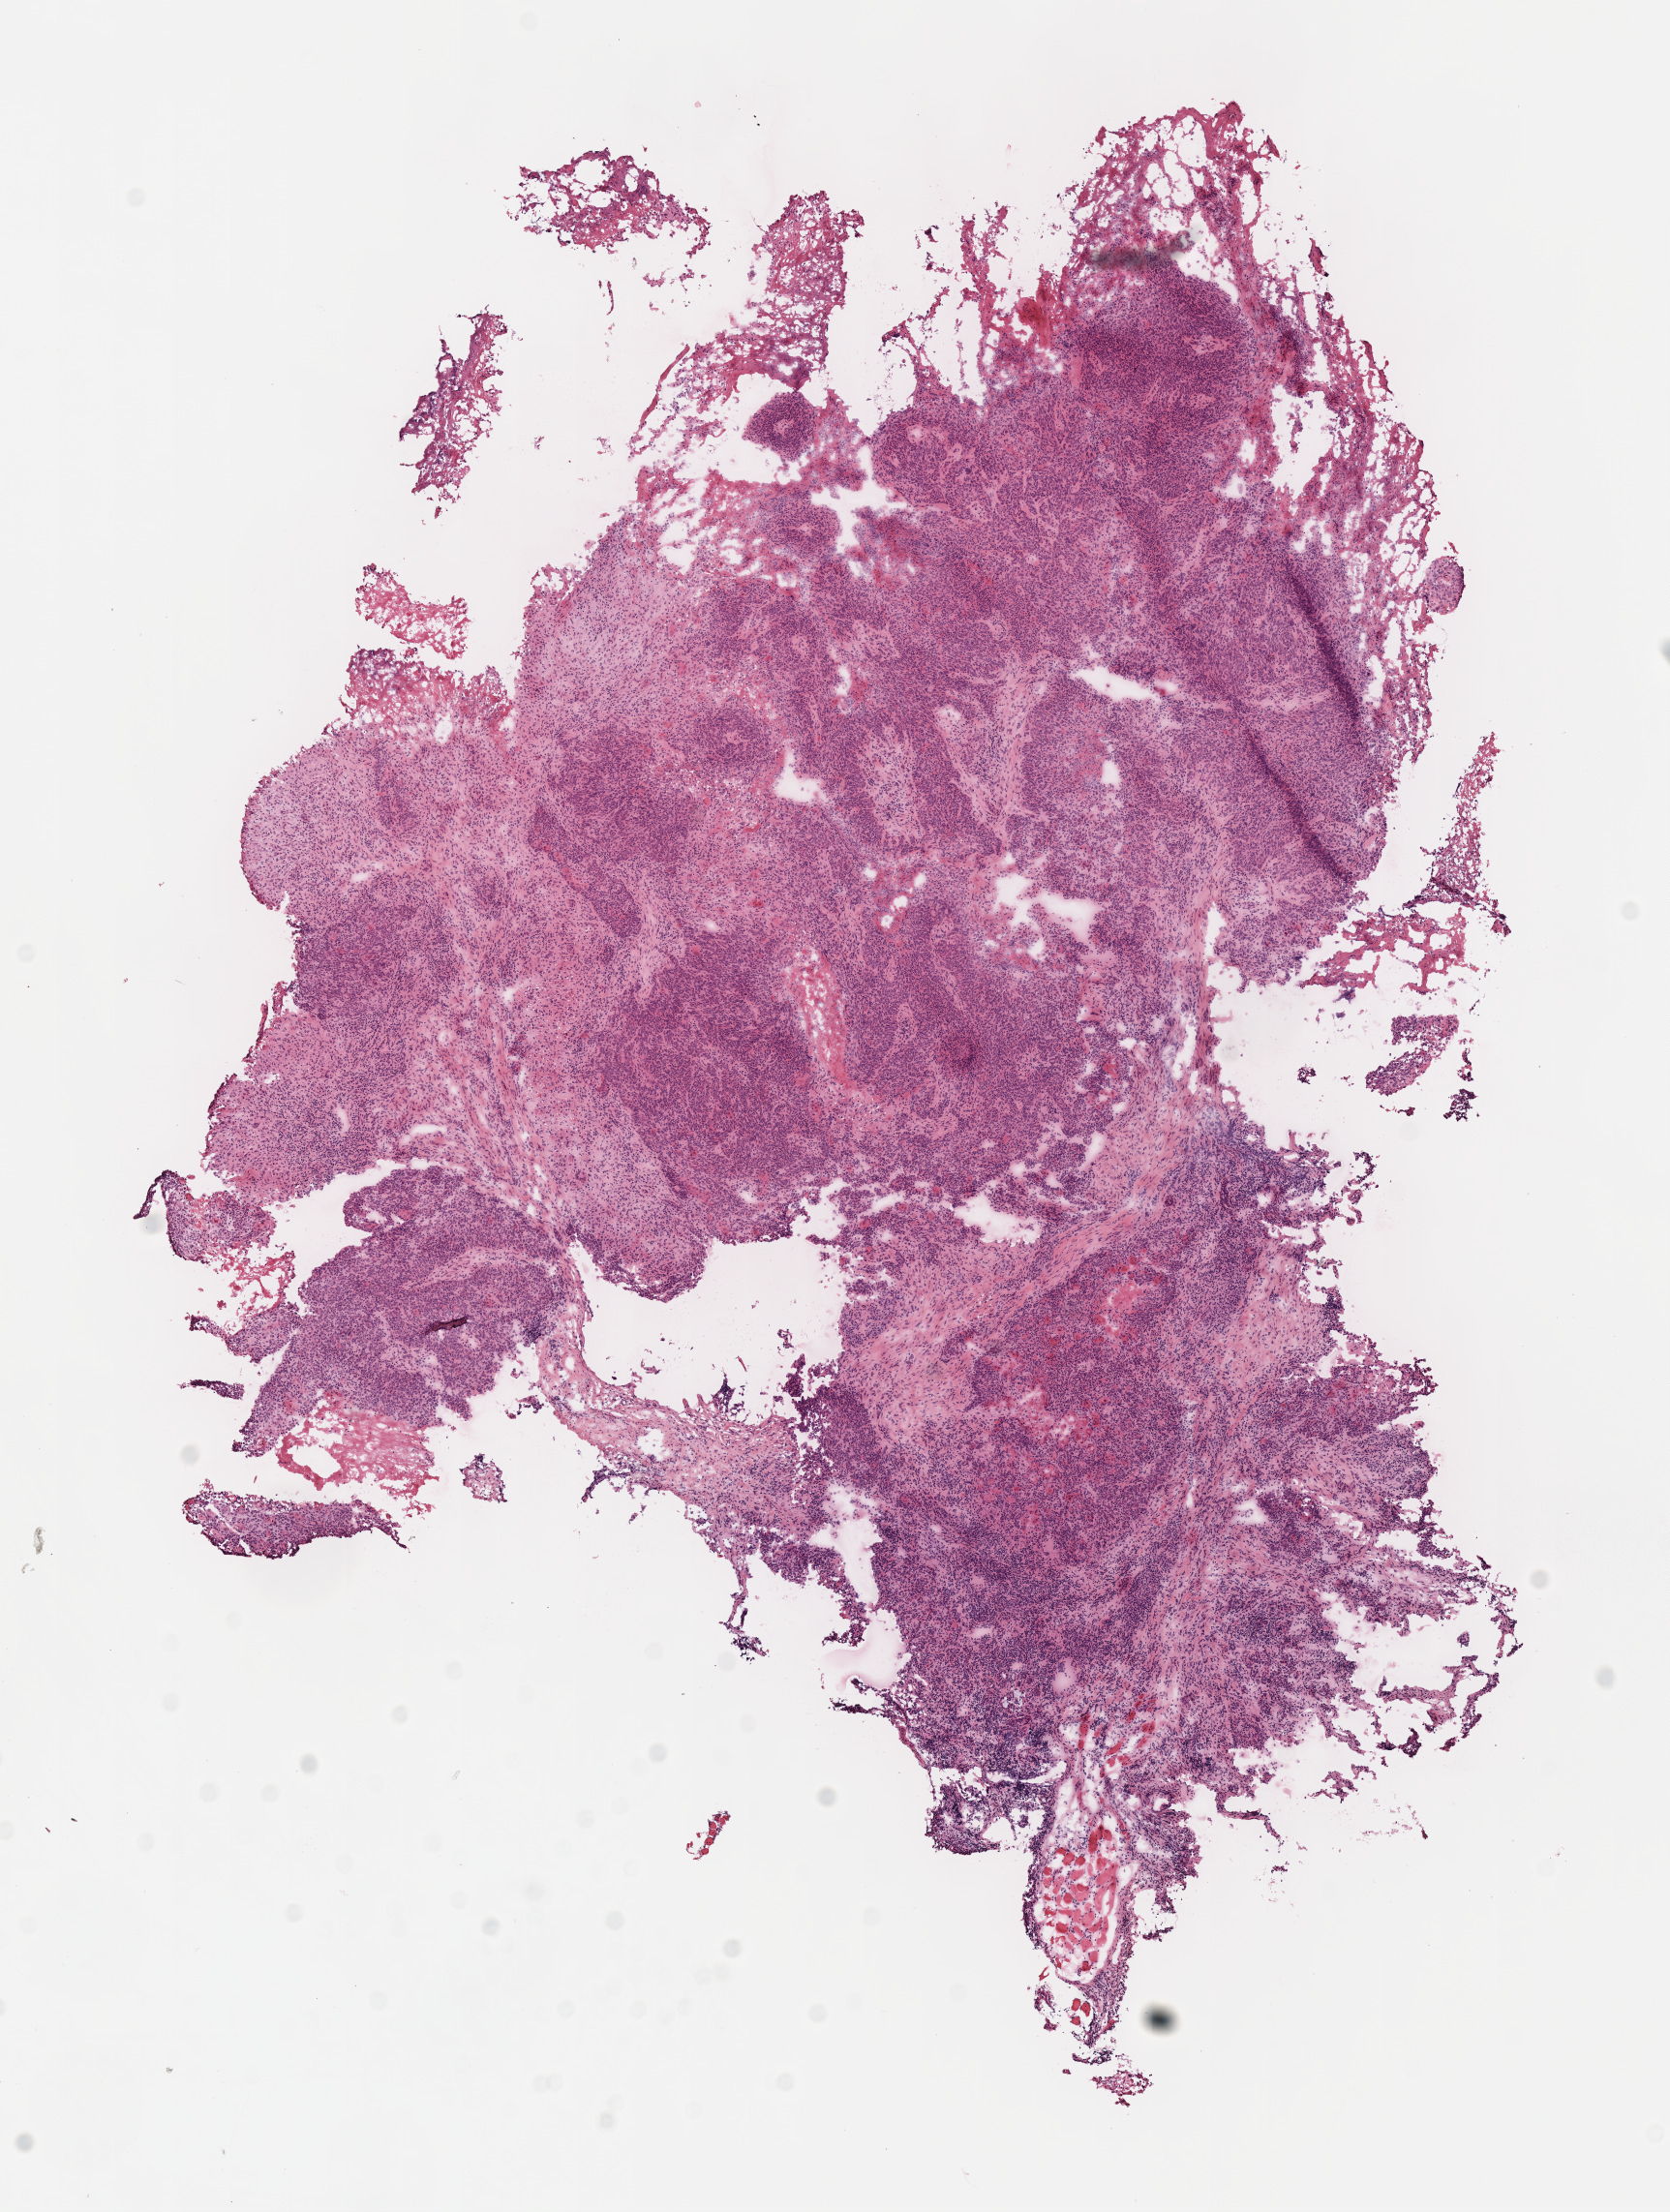
H&E whole-slide image, low-resolution overview of the scanned area, about 6.8 x 9.0 mm (from a 40x scan). Frozen section from the top of the tissue portion. Primary tumour sample from the head and neck. Male patient; age at initial diagnosis 51 years. Histologic grade: G4 (undifferentiated). Pathologist review of this section (percent, as recorded): tumour cells 83%, tumour nuclei 80%, normal cells 0%, stromal cells 15%, necrosis 2%. Inflammatory infiltration, as recorded: lymphocyte infiltration 15%.
- pathologic diagnosis: Squamous cell carcinoma, NOS
- laterality: left